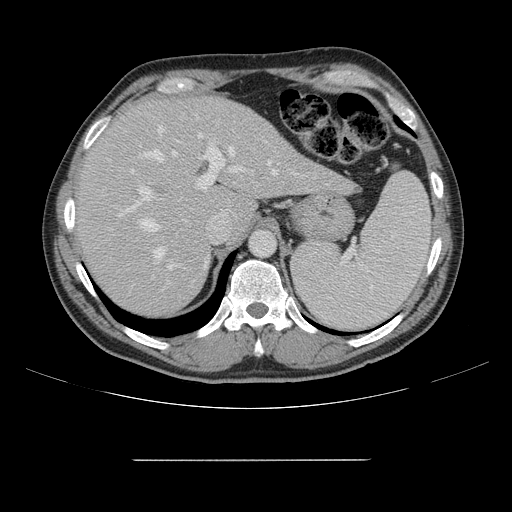
Contrast-enhanced abdominal CT, one axial slice; position 112 of 164 along the scan axis; 120 kVp; intravenous contrast given; soft-tissue window (W 400 / L 40 HU); 2.5 mm slice thickness; 512 × 512 image matrix, field of view 404 × 404 mm. Male patient, age 54 years. Case-level facts recorded for this patient, not image findings: diagnosis: colorectal cancer liver metastases, imaged before liver resection; multiple liver metastases: yes; largest metastasis: 1 cm; disease in both lobes: no.
Structures marked on this image (expert manual segmentation):
- hepatic veins: box from (x=110, y=127) to (x=278, y=259) px
- liver: (x=77, y=98)–(x=349, y=317)
- planned liver remnant (the part of the liver to remain after resection): (x=77, y=98)–(x=245, y=316)
- portal vein (with intrahepatic branches): (x=119, y=128)–(x=242, y=291)